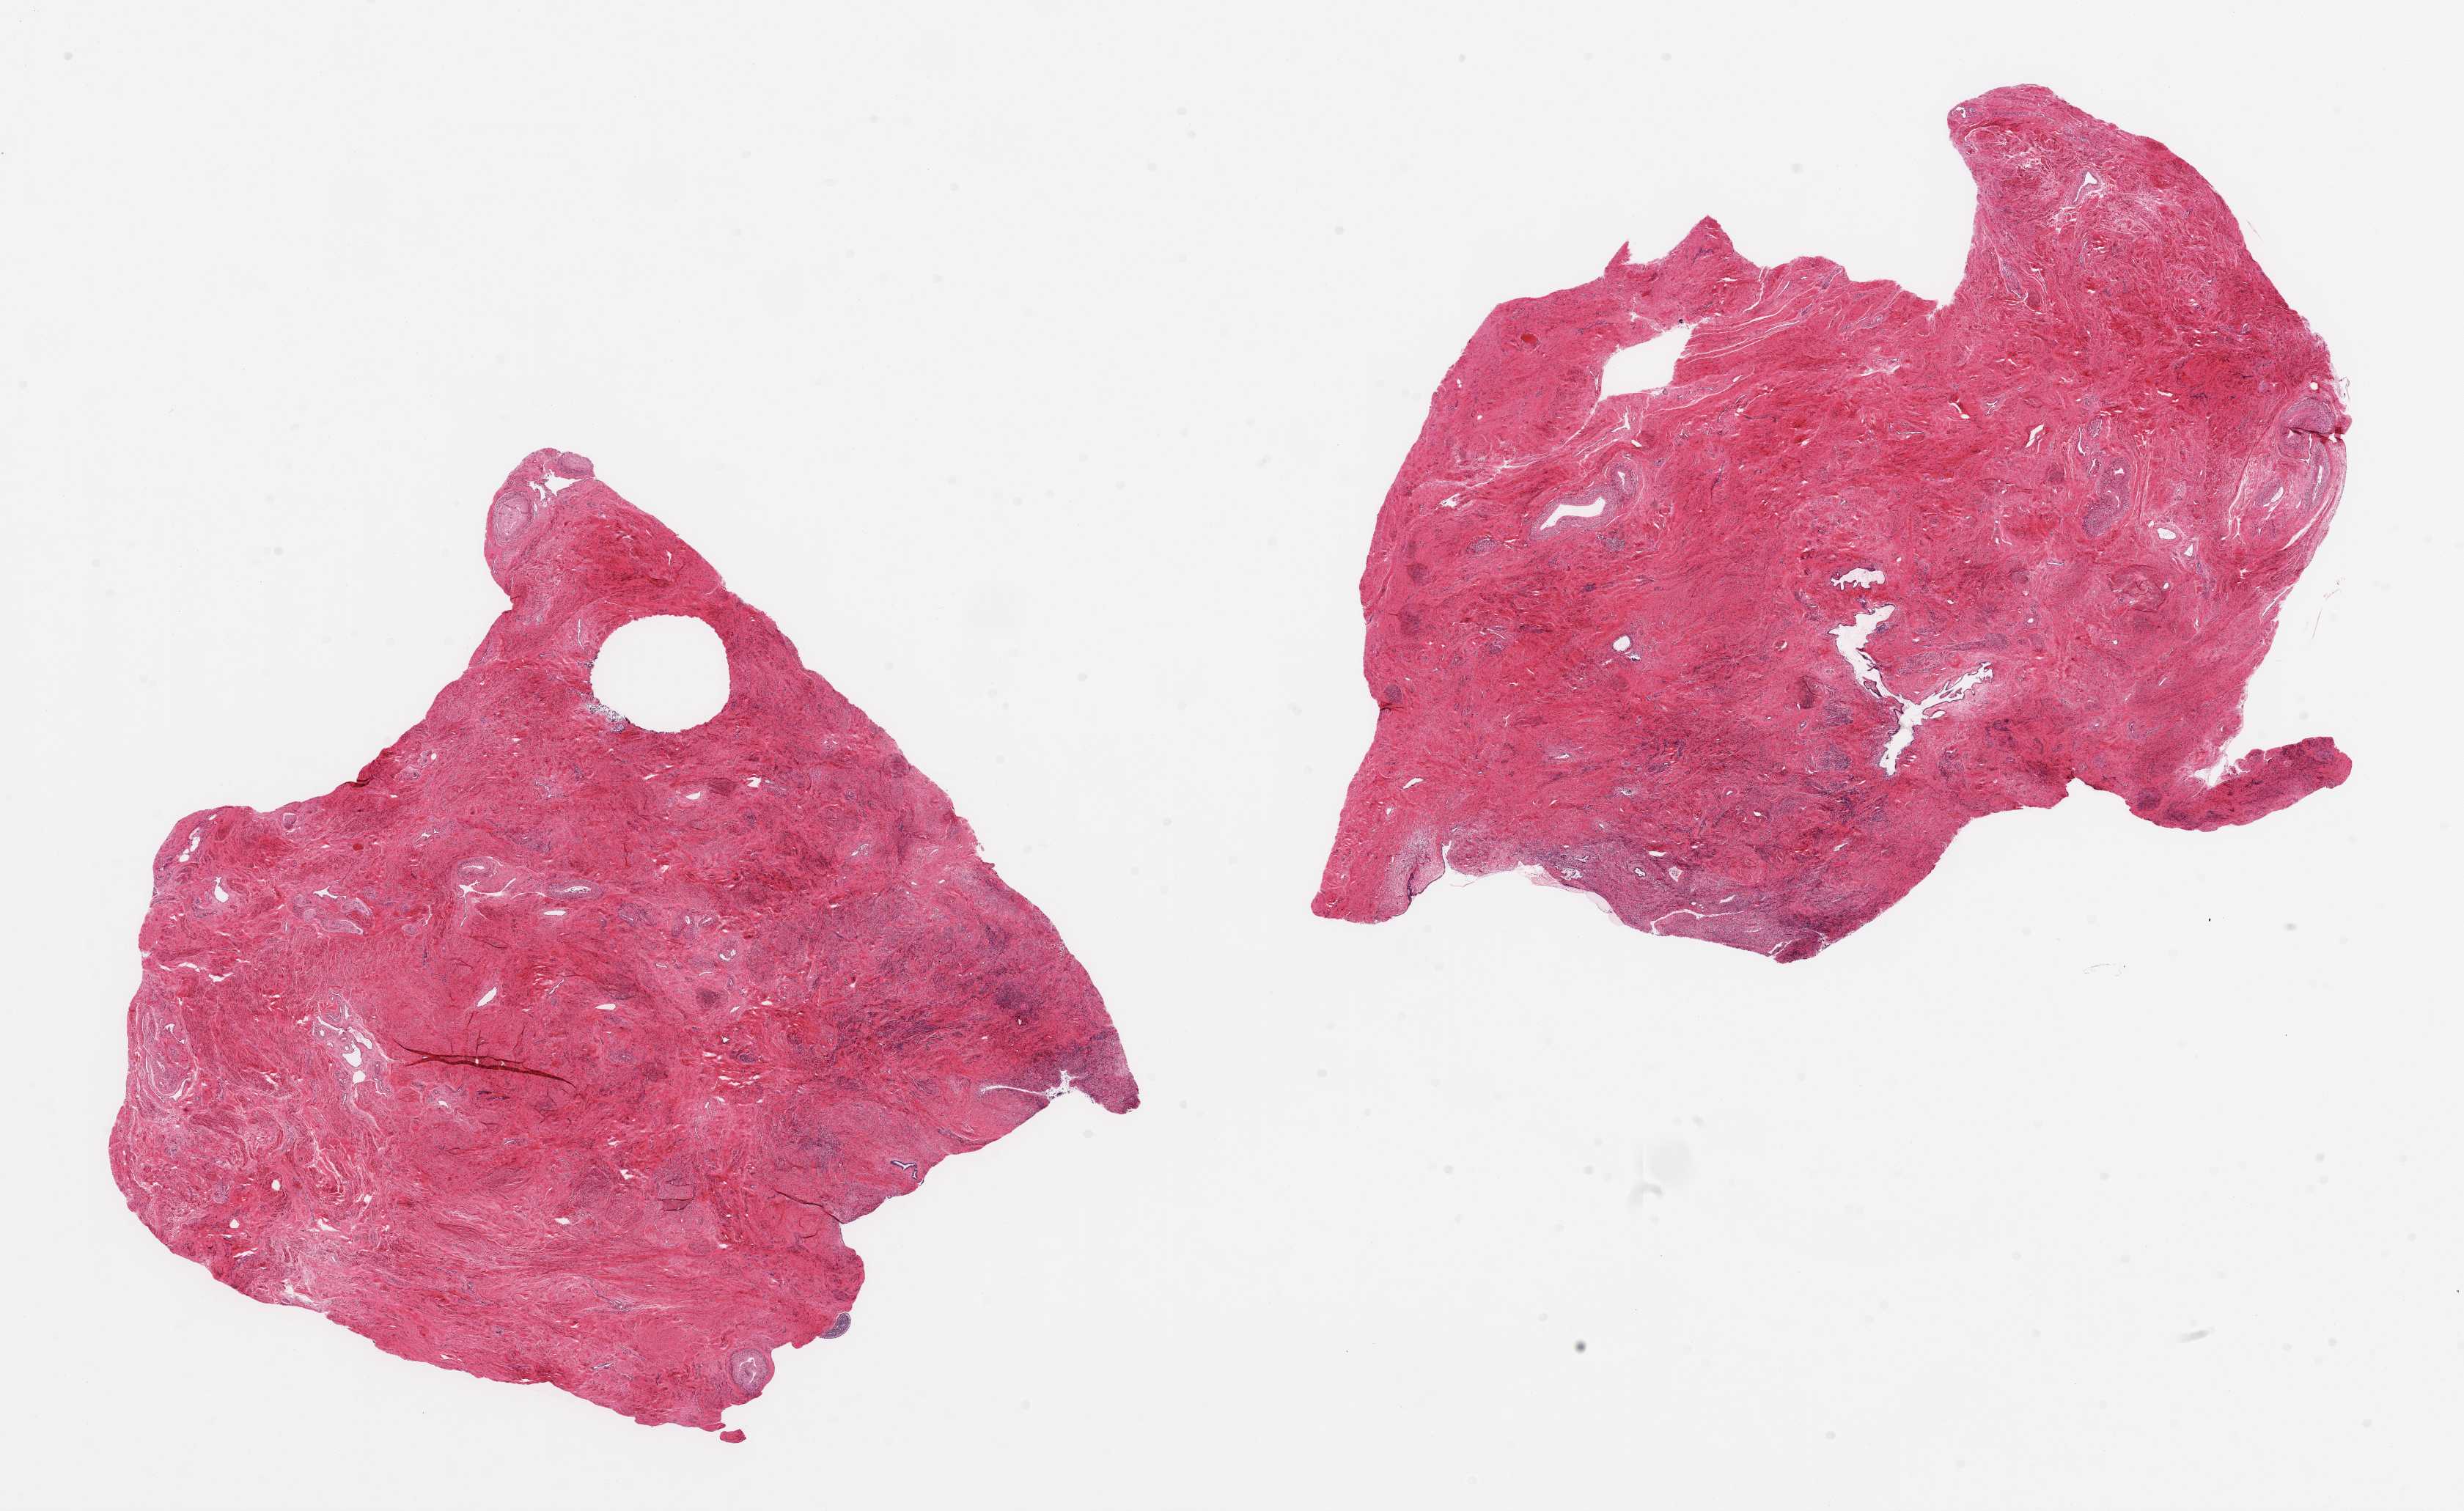
Digitized hematoxylin and eosin (H&E)-stained section, brightfield, shown as a low-resolution overview of the whole scanned area (about 26.6 x 16.3 mm). PAXgene-fixed, paraffin-embedded tissue. Sampled site (target tissue): uterus. Donor tissue sample. Female donor.
Pathologist's review note for this sample: 2 pieces; >90% is myometrium, small portion atrophic emdometrium.